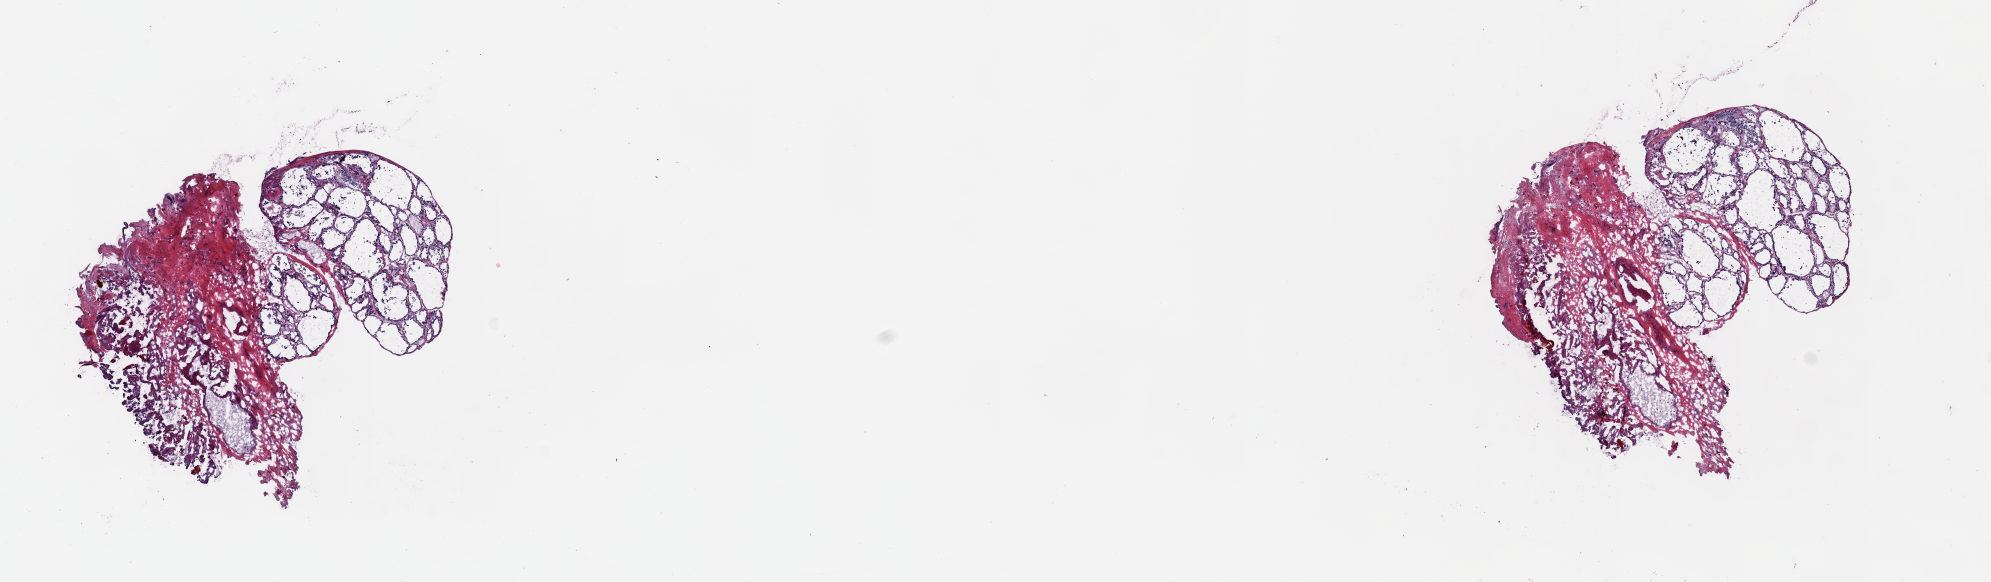
H&E whole-slide image, low-resolution overview of the scanned area, about 15.7 x 4.6 mm; frozen section from the top of the tissue portion; thyroid, solid tissue normal (non-tumour tissue) sample. Male patient; age at initial diagnosis 15 years. Slide review estimates, as recorded: tumour cells 0%, tumour nuclei 0%, normal cells 60%, stromal cells 40%, necrosis 0%. Inflammatory infiltration, as recorded: lymphocyte infiltration 4%, monocyte infiltration 1%, neutrophil infiltration 0%.
This section: solid tissue normal (non-tumour) sample from the same patient. Patient diagnosis: Papillary adenocarcinoma, NOS (thyroid gland).